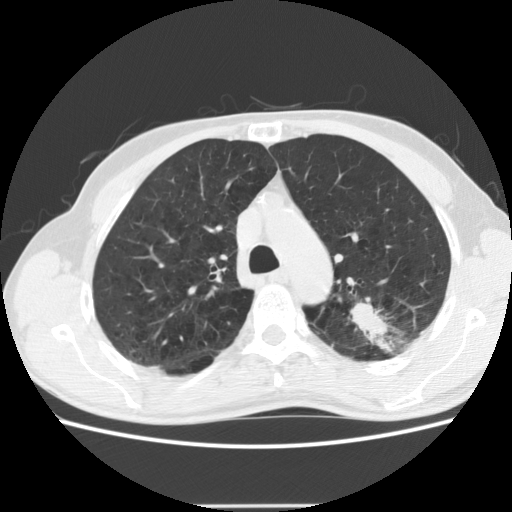
Chest CT (low-dose screening protocol), one axial image, baseline screening round, lung window (W 1500 / L -600 HU), 2.5 mm slice thickness, standard (soft-tissue) reconstruction kernel (STANDARD), slice 50 of 191 in the series, 512 × 512 image matrix, field of view 352 × 352 mm. Male participant, aged 64 years at enrolment.
Expert reader's lesion annotation, bounding box <339,281,439,360> (left, top, right, bottom; pixels). The exam's reader record, not a measurement of the box and not confirmed to be the same lesion: non-calcified nodule or mass ≥4 mm, left upper lobe, 27 × 19 mm, poorly defined margins, soft tissue attenuation. Later outcome: lung cancer diagnosed 23 days after this screen — adenocarcinoma, NOS, left upper lobe, moderately differentiated (G2), stage IA (AJCC 6th edition), 29 mm at pathology.